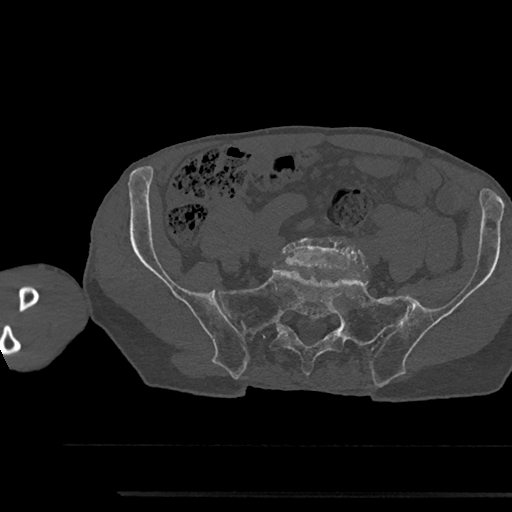
CT including the spine, one axial slice; slice 295 of 797 in the series (ordered by position); reconstruction kernel Br40s/3; 120 kVp; bone window (W 1800 / L 400 HU); 512 × 512 image matrix. Patient: male, 79 years. Case-level facts recorded for this patient, not image findings: primary cancer: prostate.
Annotated regions visible in this slice (semi-automatic segmentation, software-assisted and operator-edited):
- L5 vertebra: box from (x=281, y=237) to (x=367, y=271) px